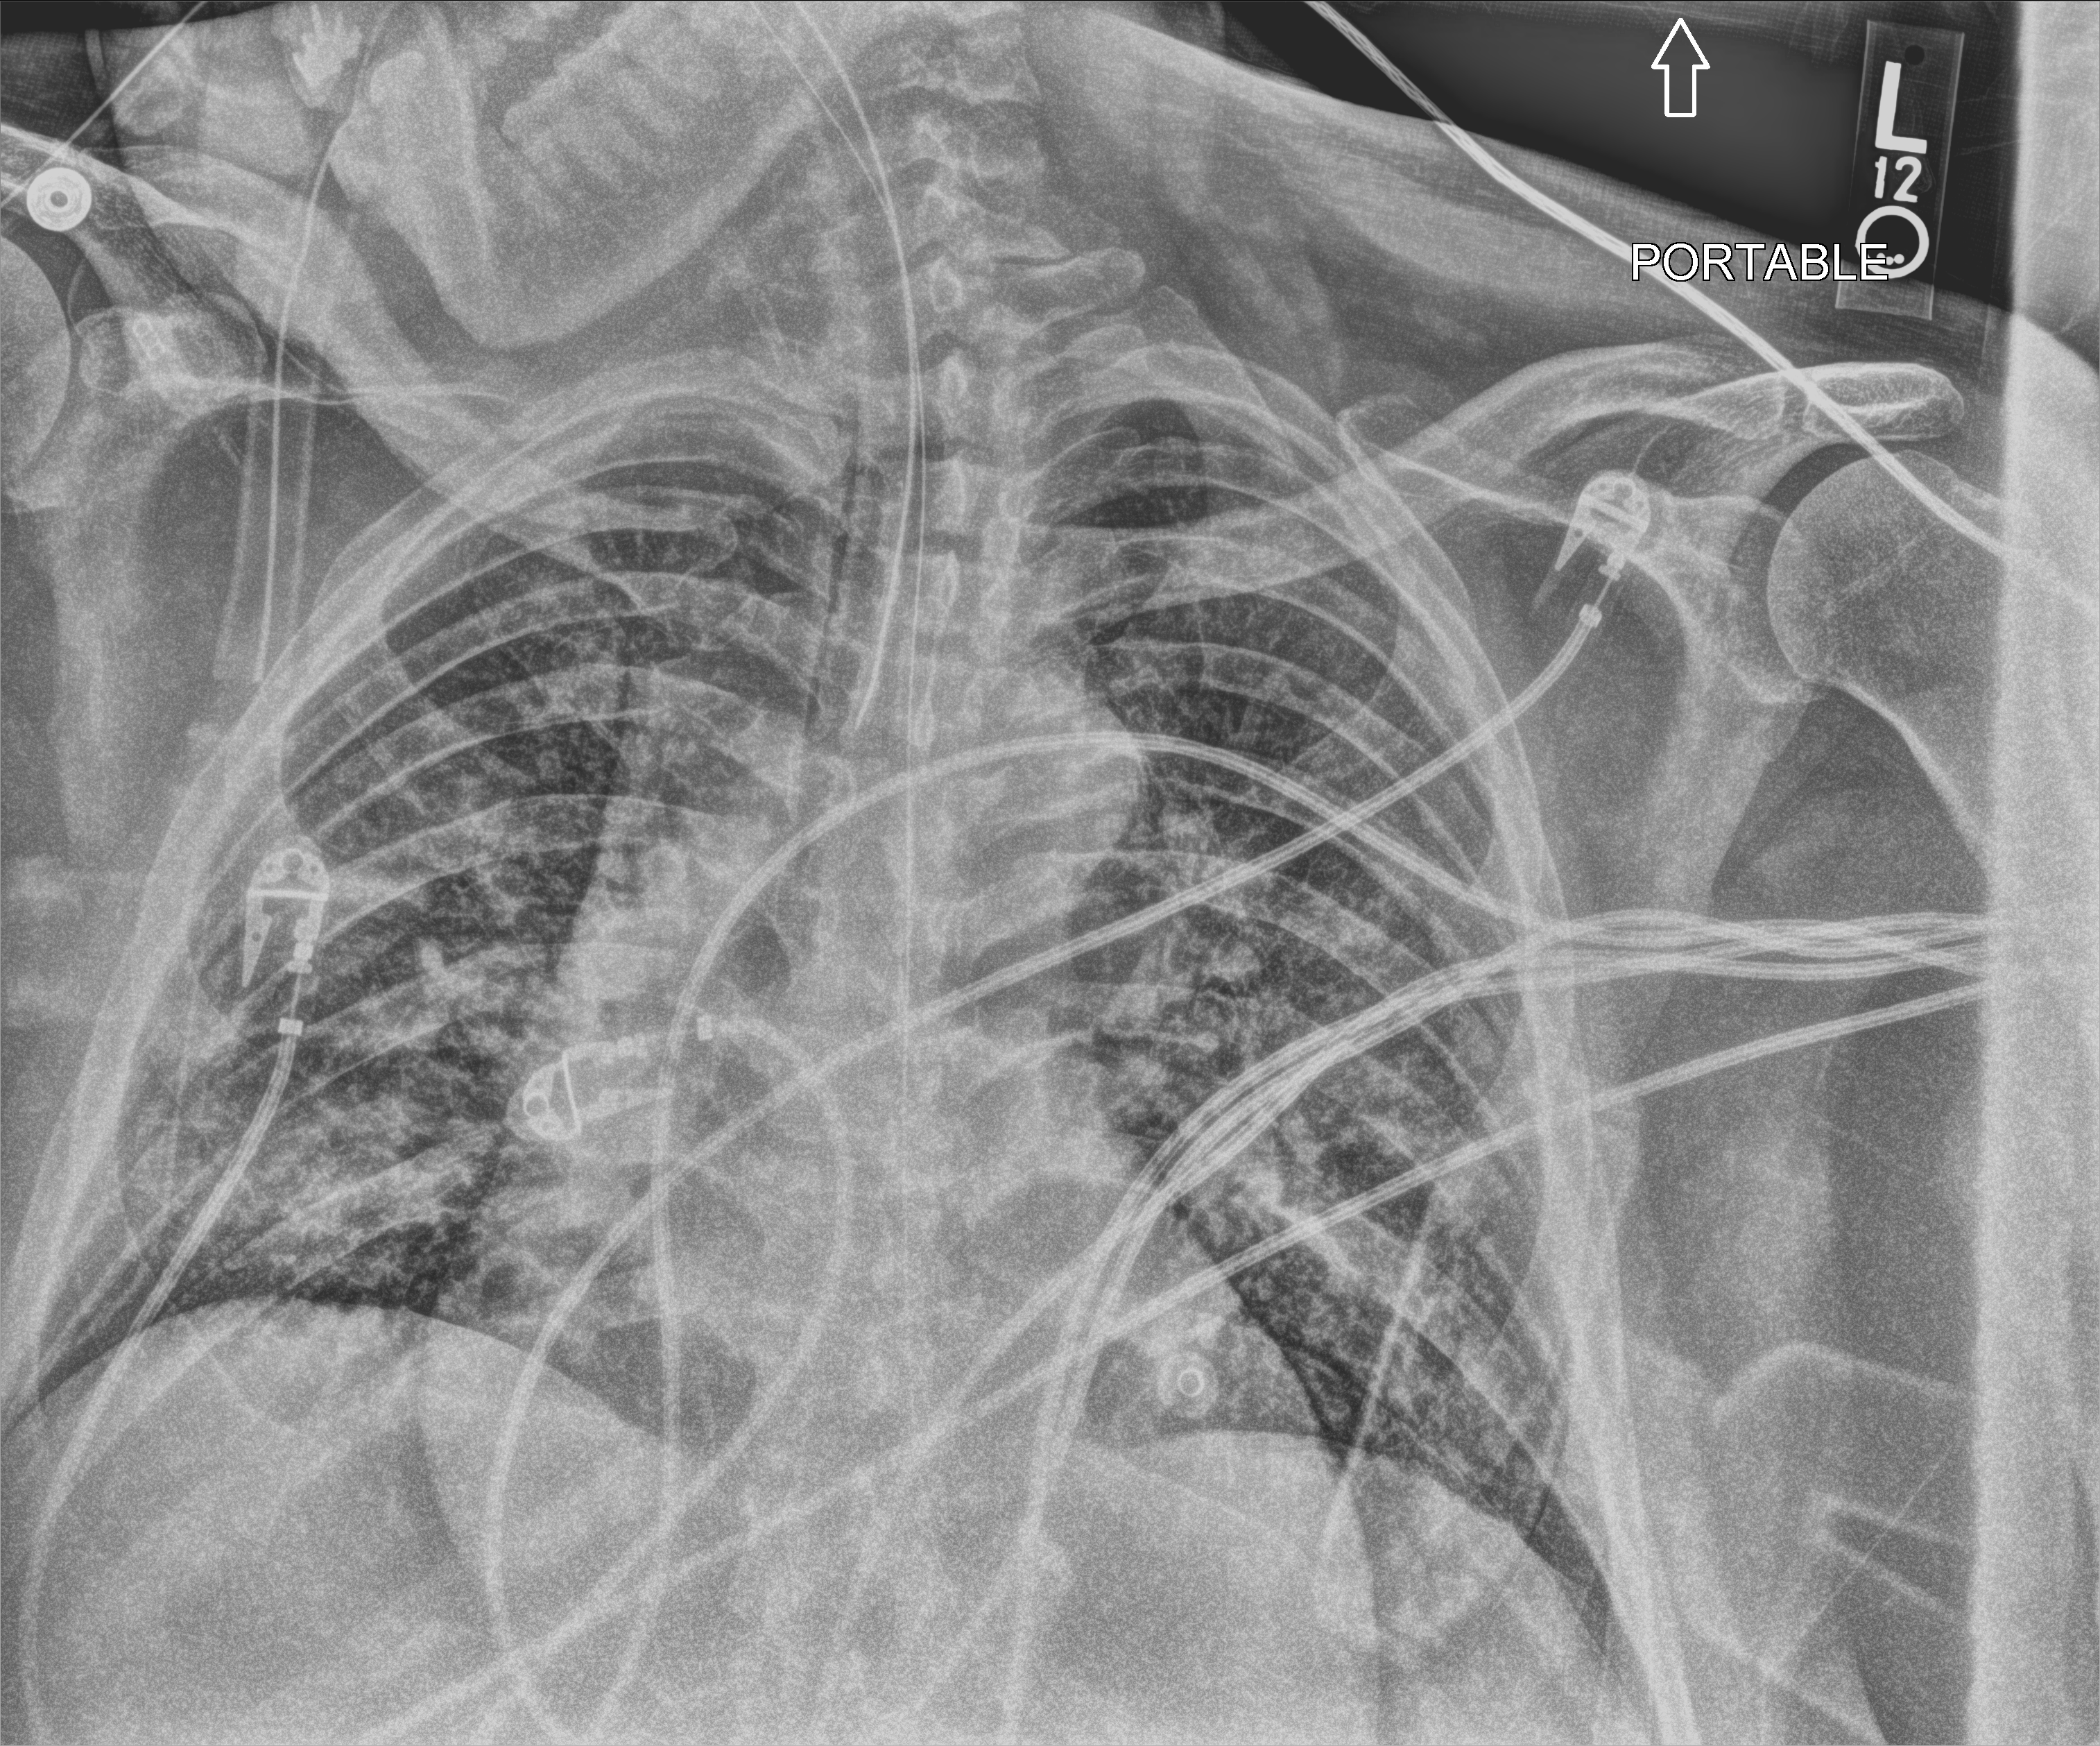
Chest X-ray (portable), anteroposterior (AP) projection. Male patient hospitalised with COVID-19, age 60–74 years.
Admission-level facts for this patient (not findings on this image; timing relative to this image not recorded): mechanically ventilated during this hospital stay: yes; other chronic lung disease (admission record): no; admitted to intensive care during this hospital stay: yes.